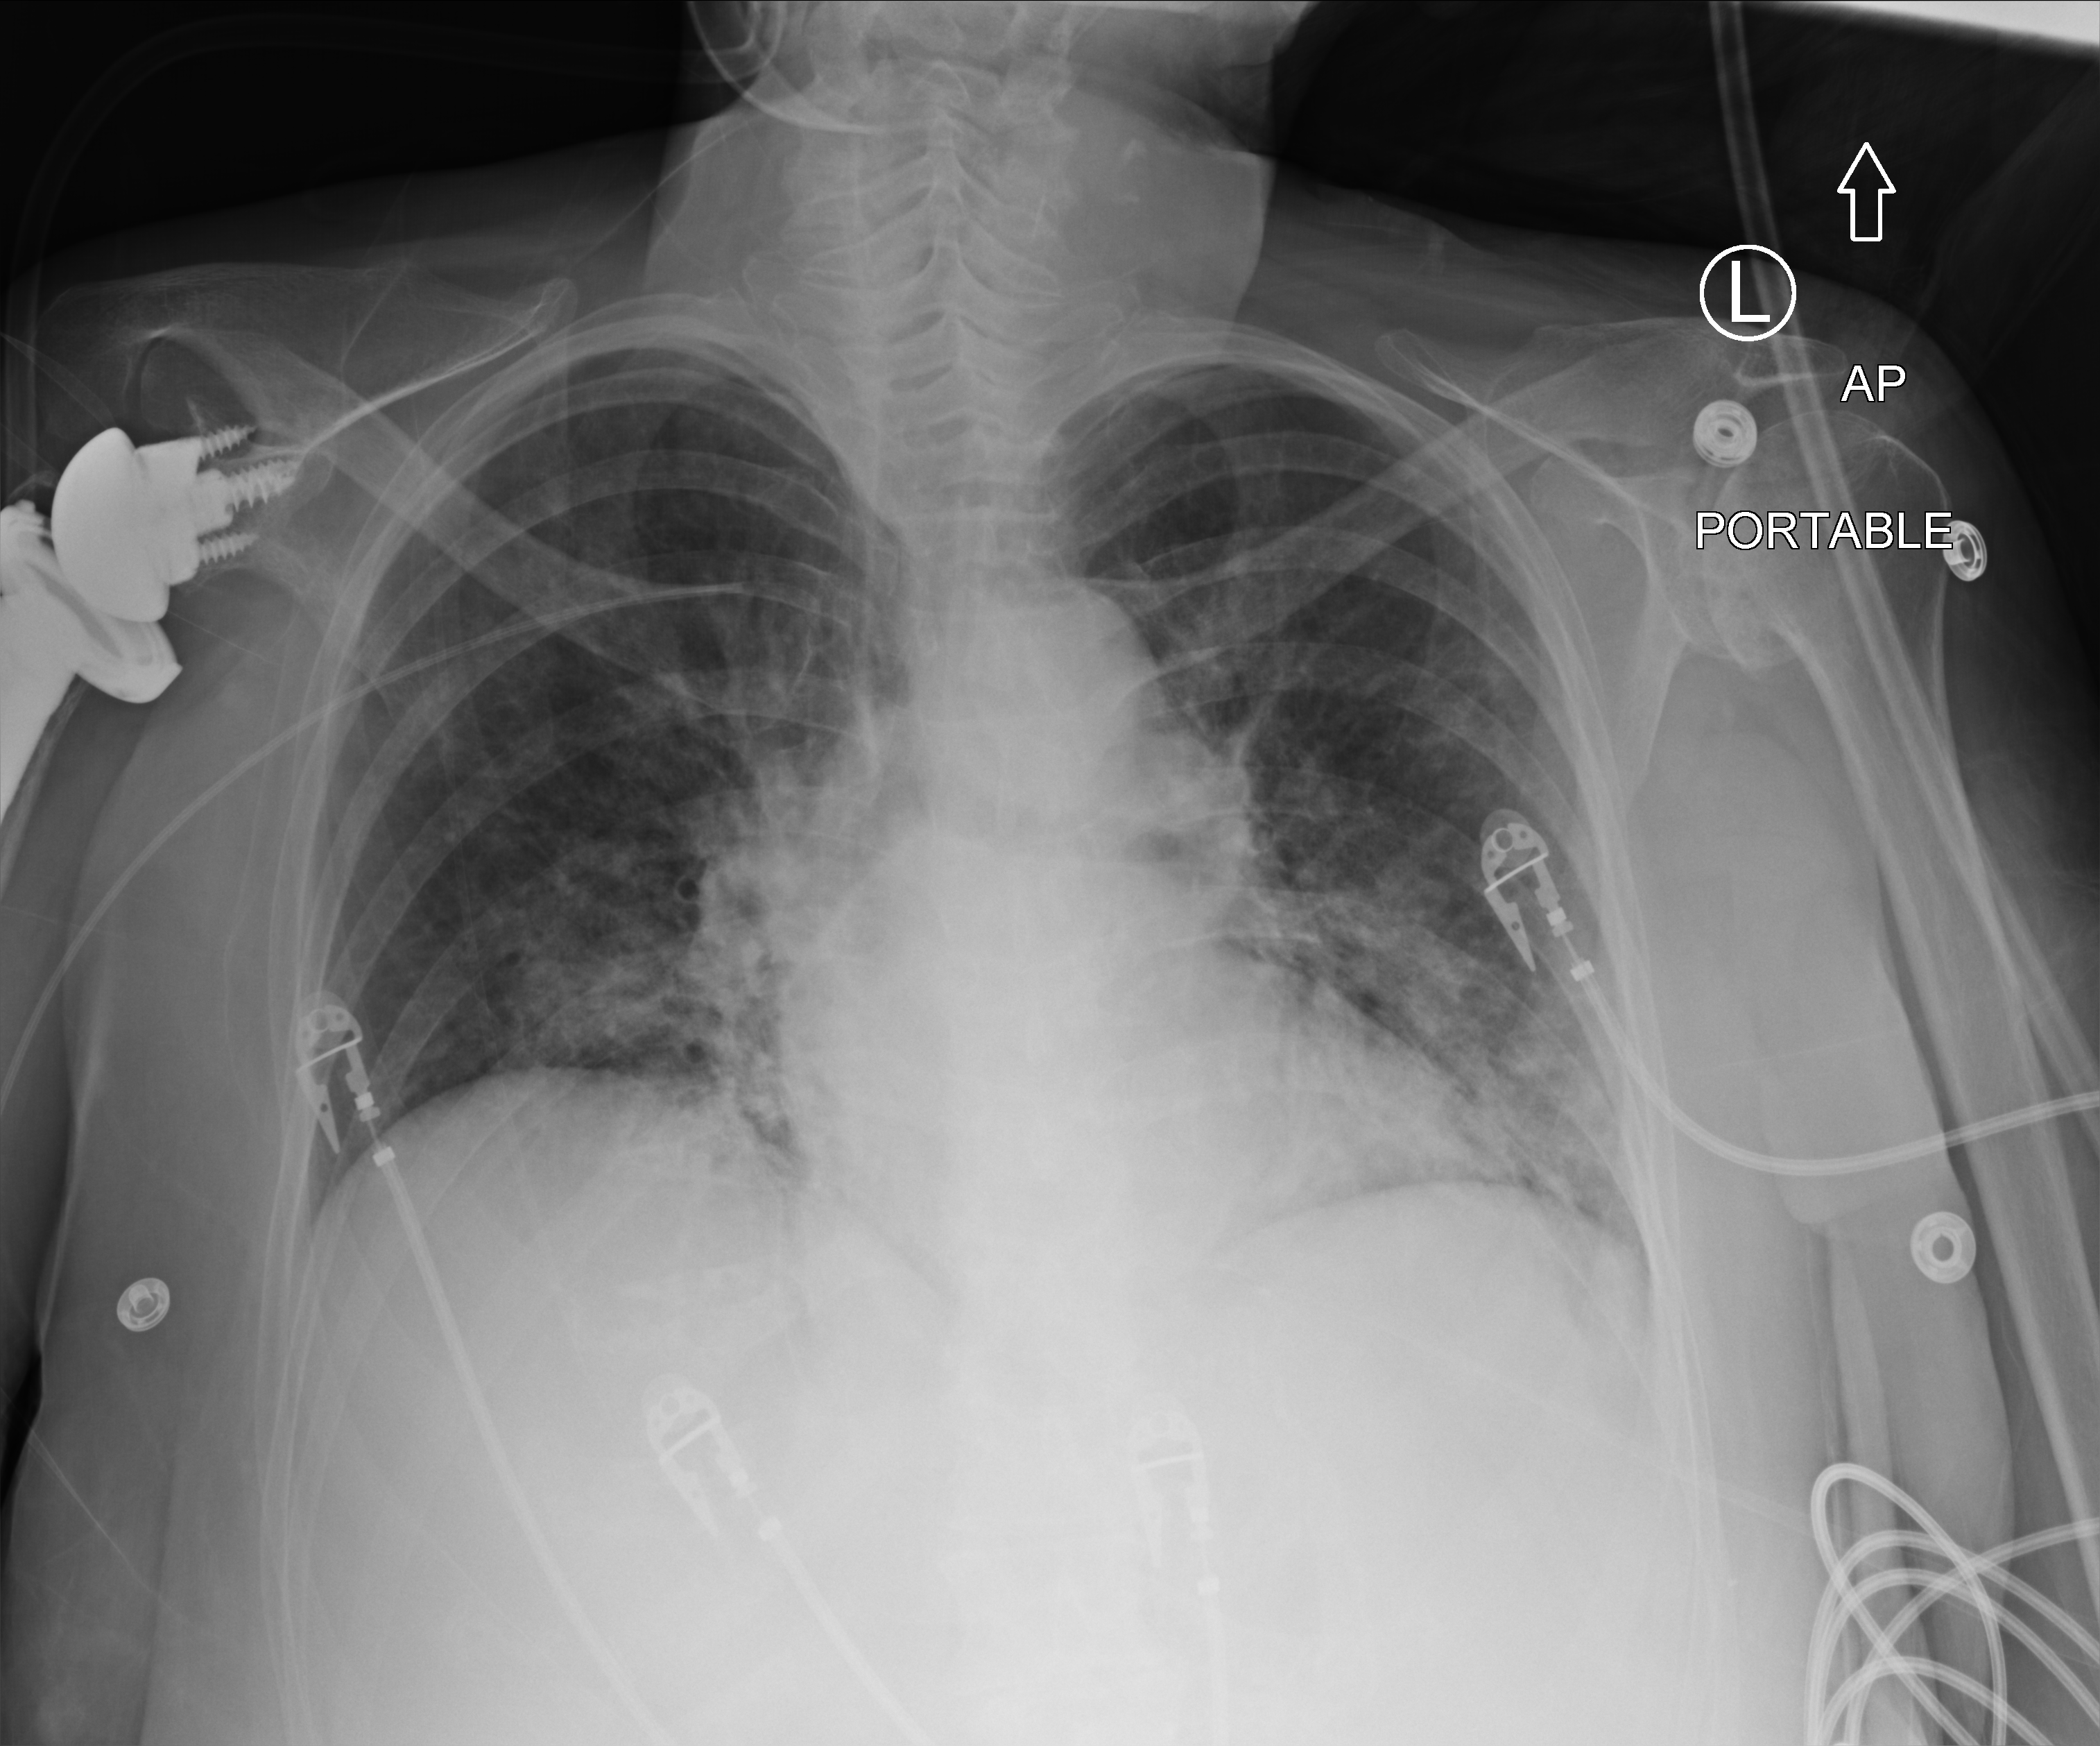
Chest X-ray (portable); anteroposterior (AP) projection. Patient hospitalised with COVID-19; female, aged 60–74 years.
Hospital-stay facts (about this admission, not read from this image; timing relative to this image not recorded): length of hospital stay: 27 days; admitted to intensive care during this hospital stay: yes.